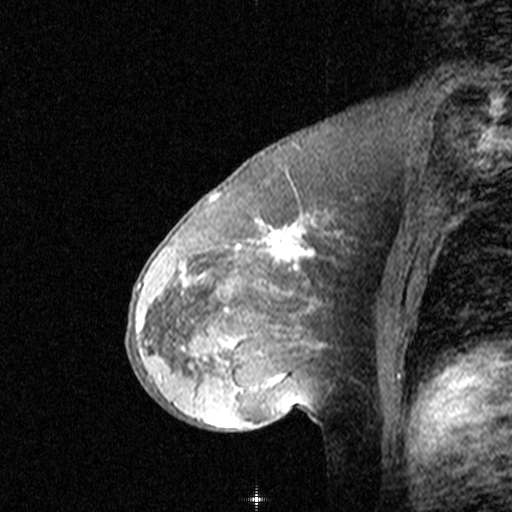
Breast MRI (dynamic contrast-enhanced), one sagittal slice. Slice 24 of 44 in the series (ordered by position). Dynamic contrast-enhanced study with each time point stored as its own series, time point 2 of 3 at this slice position (early post-contrast, ordered by acquisition time). 1.5 T. TE 4.5 ms, TR 11 ms. 512 × 512 image matrix. Patient: female, 46 years. From the clinical record (not read from this slice): setting: breast cancer imaged before/during neoadjuvant chemotherapy; receptor status: HER2-positive.
Annotated regions visible in this slice (semi-automatically segmented with operator editing):
- analysis volume of interest (the breast-tissue region the enhancement analysis was run in; not a lesion): box from (x=144, y=172) to (x=359, y=393) px
- tumour enhancement mask (voxels above the 90 % enhancement threshold inside the analysis volume of interest): (x=144, y=221)–(x=340, y=393)